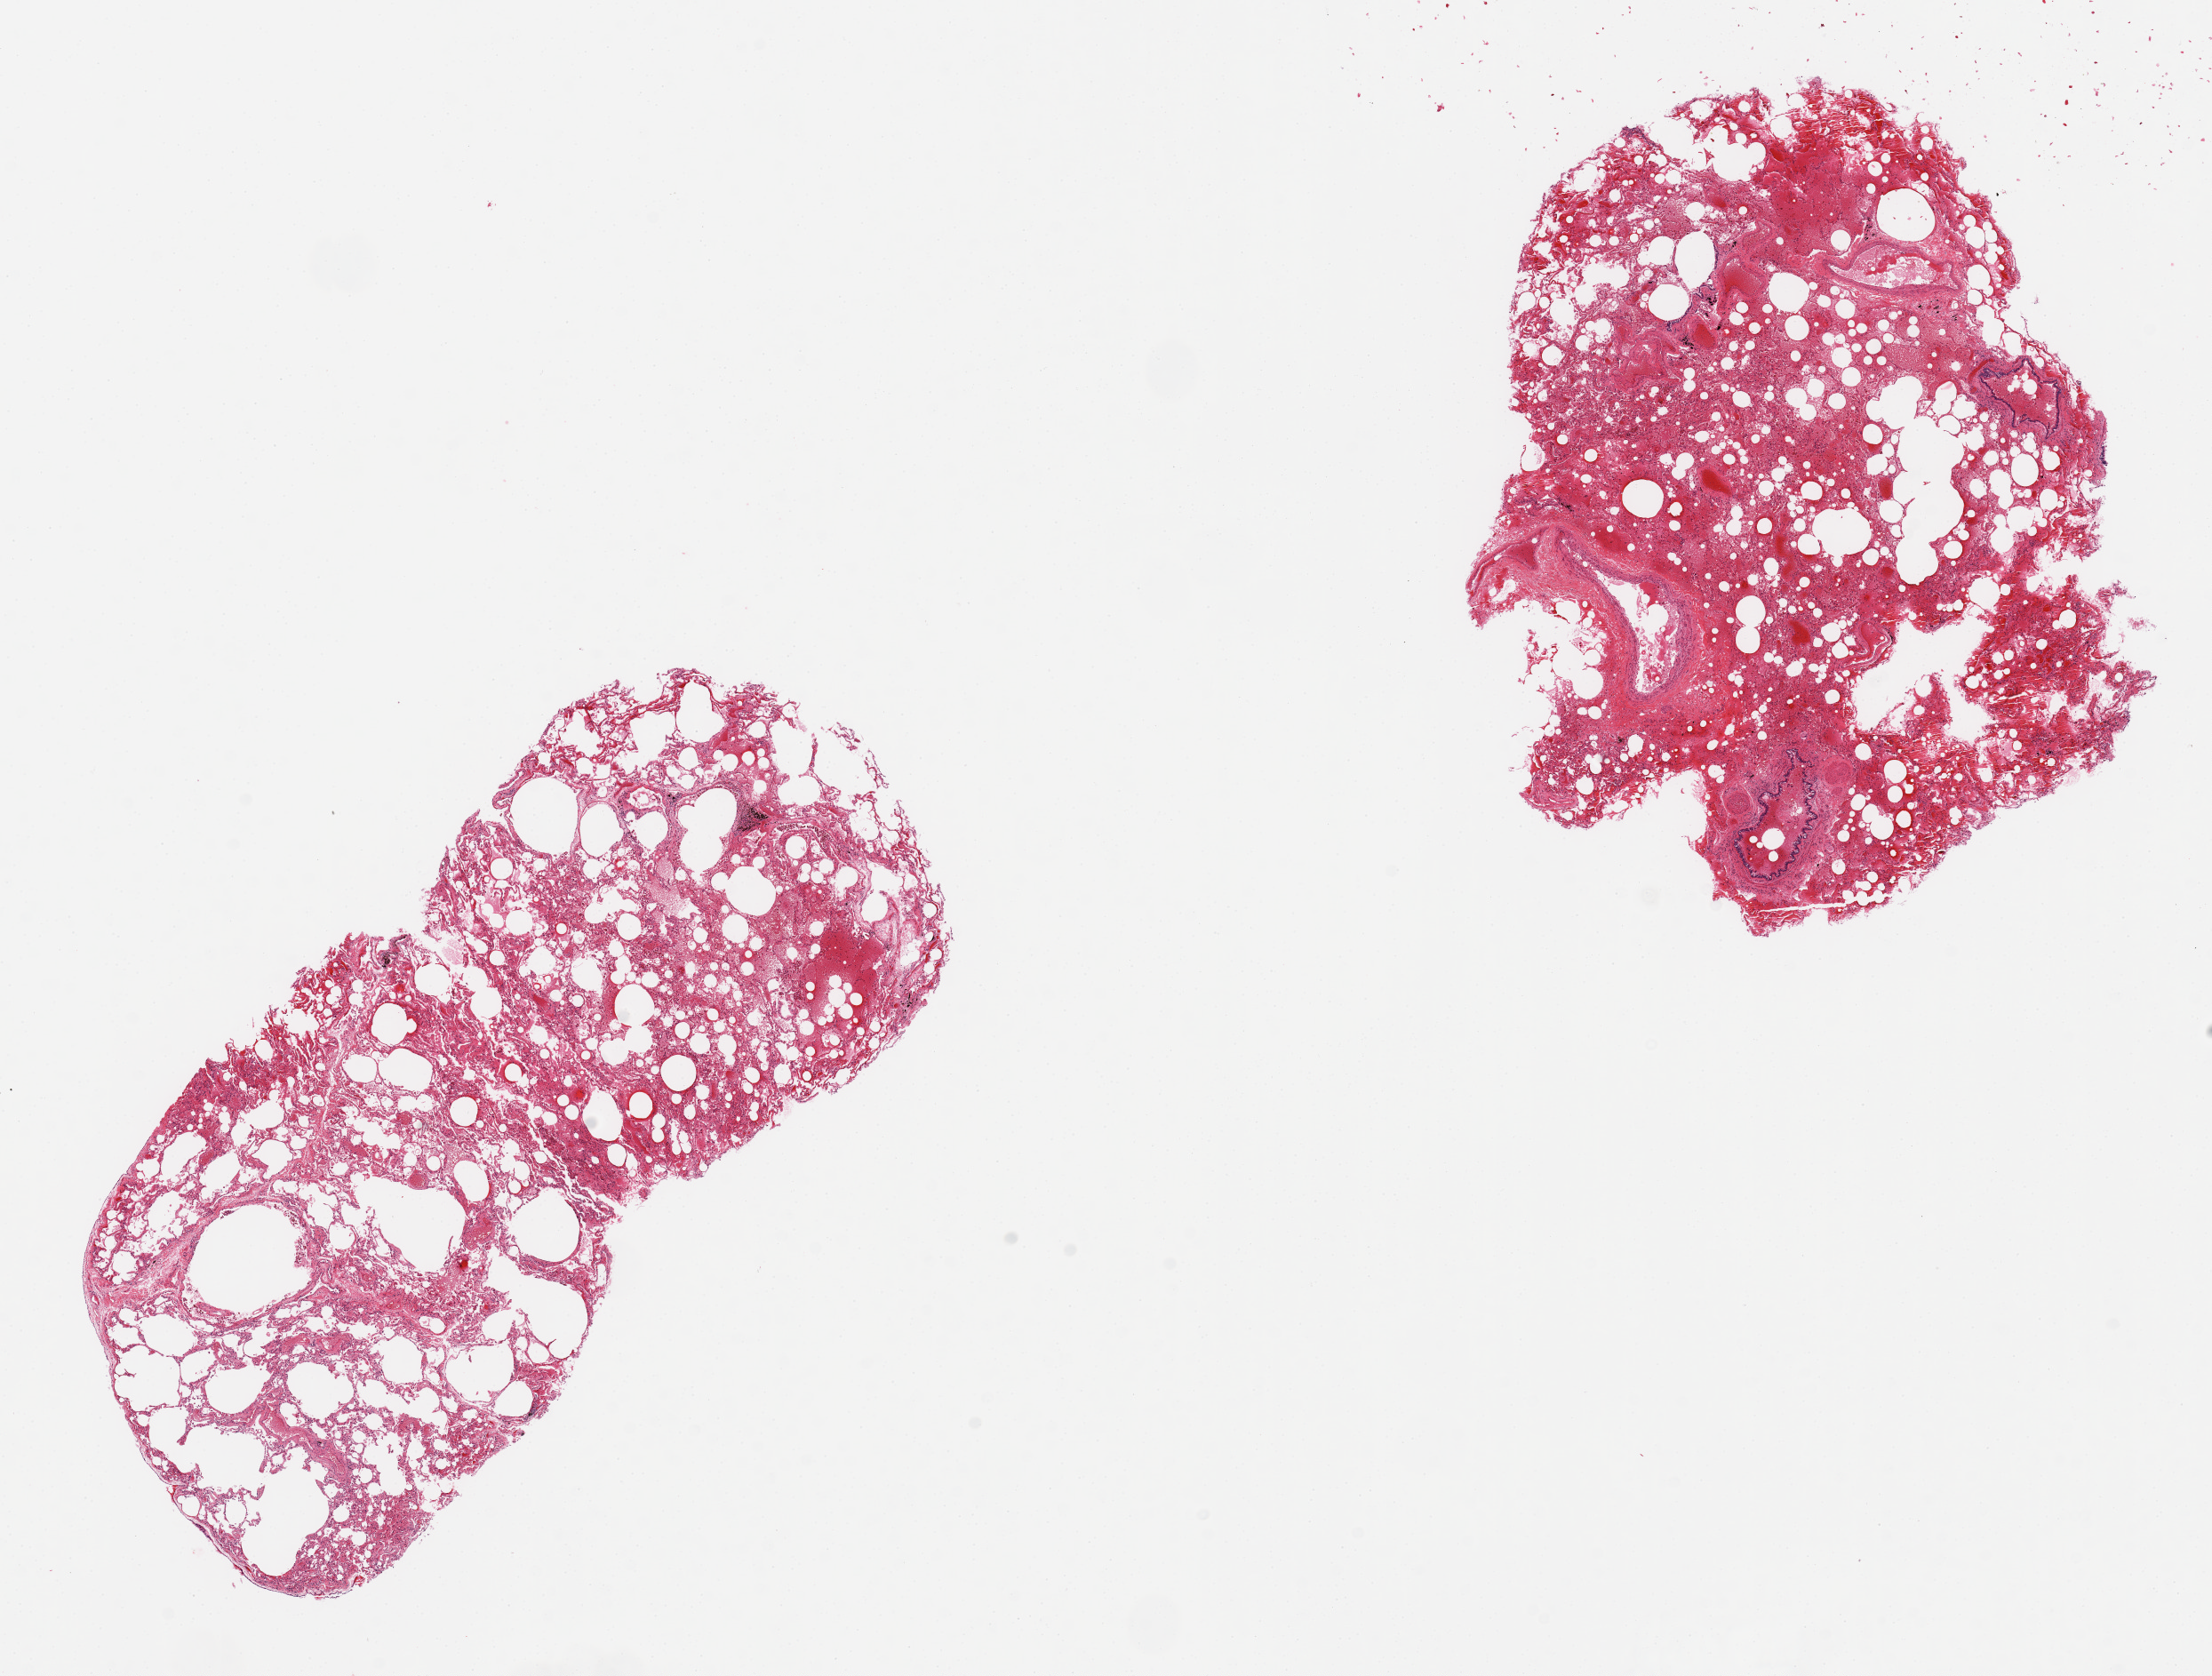
Digitized hematoxylin and eosin (H&E)-stained section, a low-resolution overview of the entire scanned area, about 19.7 x 14.9 mm; PAXgene-fixed paraffin-embedded (PFPE) section; section of lung (target tissue); donor tissue sample. Male donor.
* pathologist's review note for this sample: 2 pieces, moderate congestion